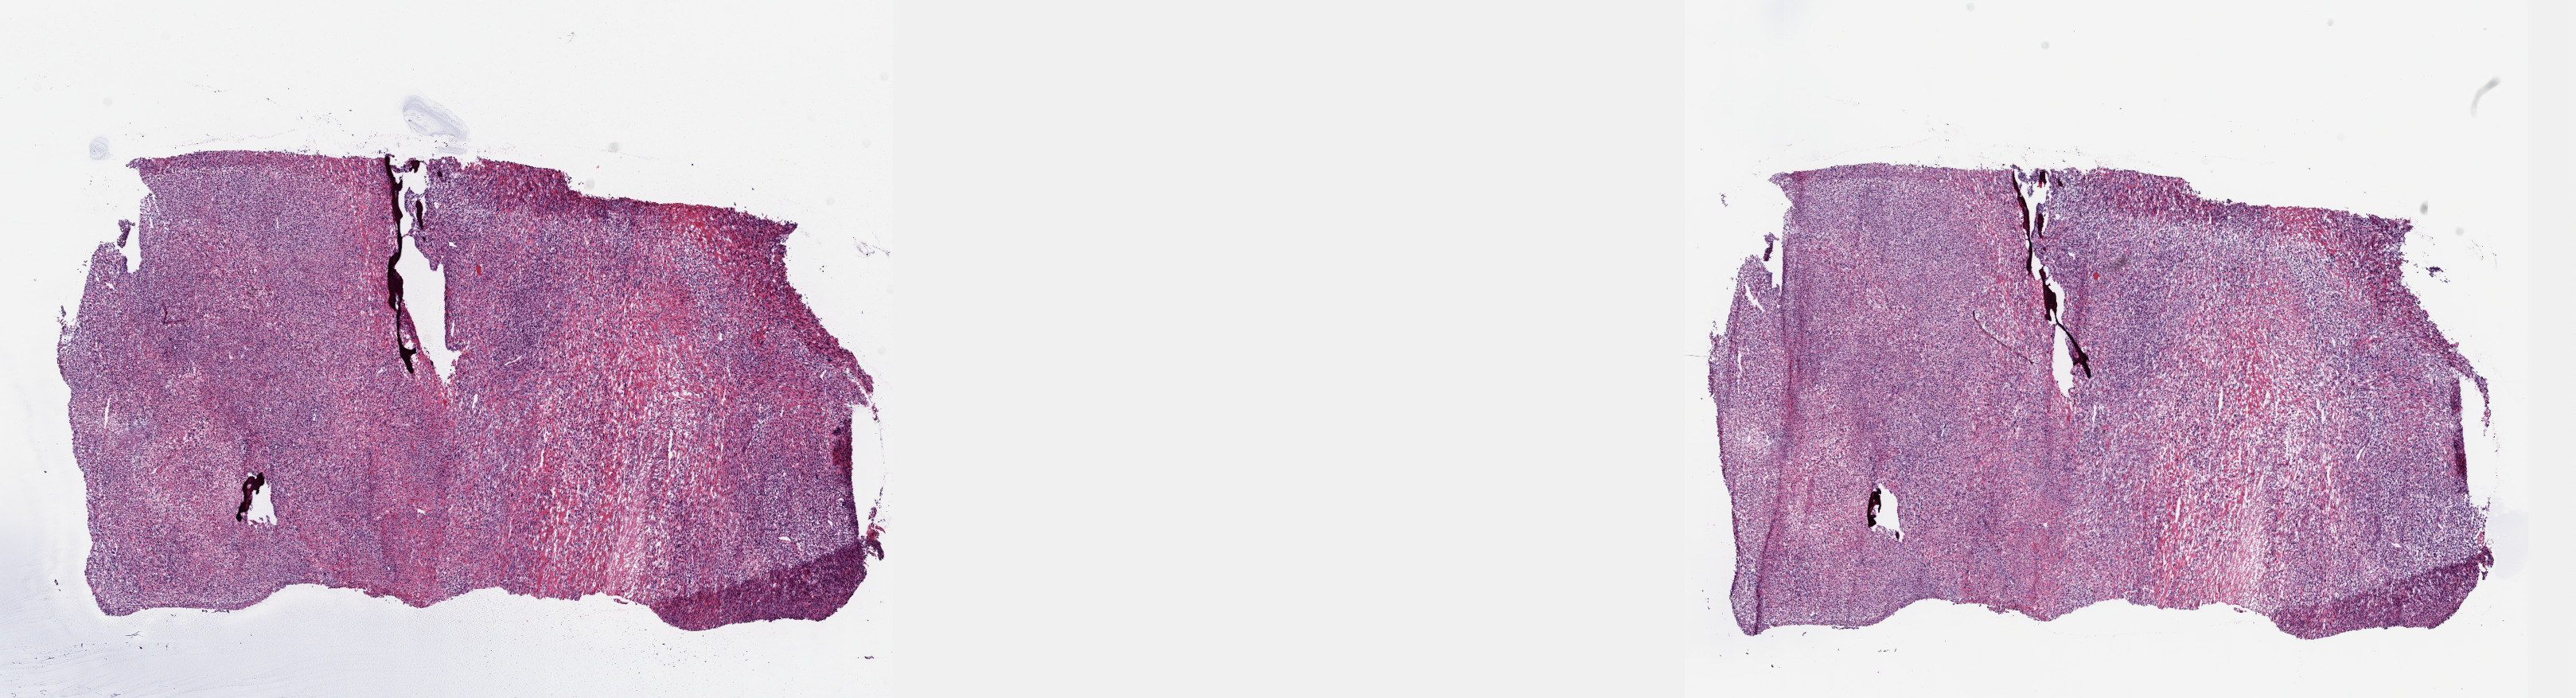
Whole-slide histology image, H&E — shown as a low-resolution overview of the whole scanned area (about 26.2 x 7.1 mm, from a 40x scan); frozen section; primary tumour sample from the retroperitoneum and peritoneum. Male, age 72 years at initial diagnosis. Slide review estimates, as recorded: tumour cells 85%, tumour nuclei 95%, normal cells 0%, stromal cells 15%, necrosis 0%. Inflammatory infiltration, as recorded: lymphocyte infiltration 0%, monocyte infiltration 0%, neutrophil infiltration 0%.
- histologic diagnosis: Sarcoma, NOS (retroperitoneum)